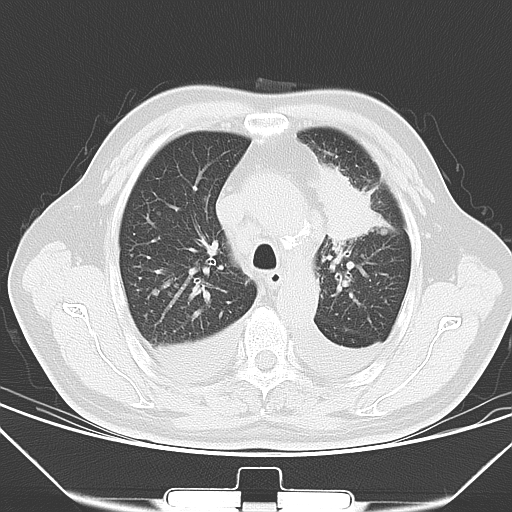
Chest CT, one axial slice. 120 kVp. Lung window (W 1500 / L -600 HU). 5 mm slice thickness. 512 × 512 image matrix, field of view 352 × 352 mm. Male patient, age 66 years. From the clinical record (not read from this slice): clinical TNM (as recorded): T1c N0 M0.
Outlined on this slice (bounding box drawn by a radiologist):
- lung tumour (recorded histology: adenocarcinoma): bounding box (x1, y1, x2, y2) in pixels: (313, 160, 392, 242)